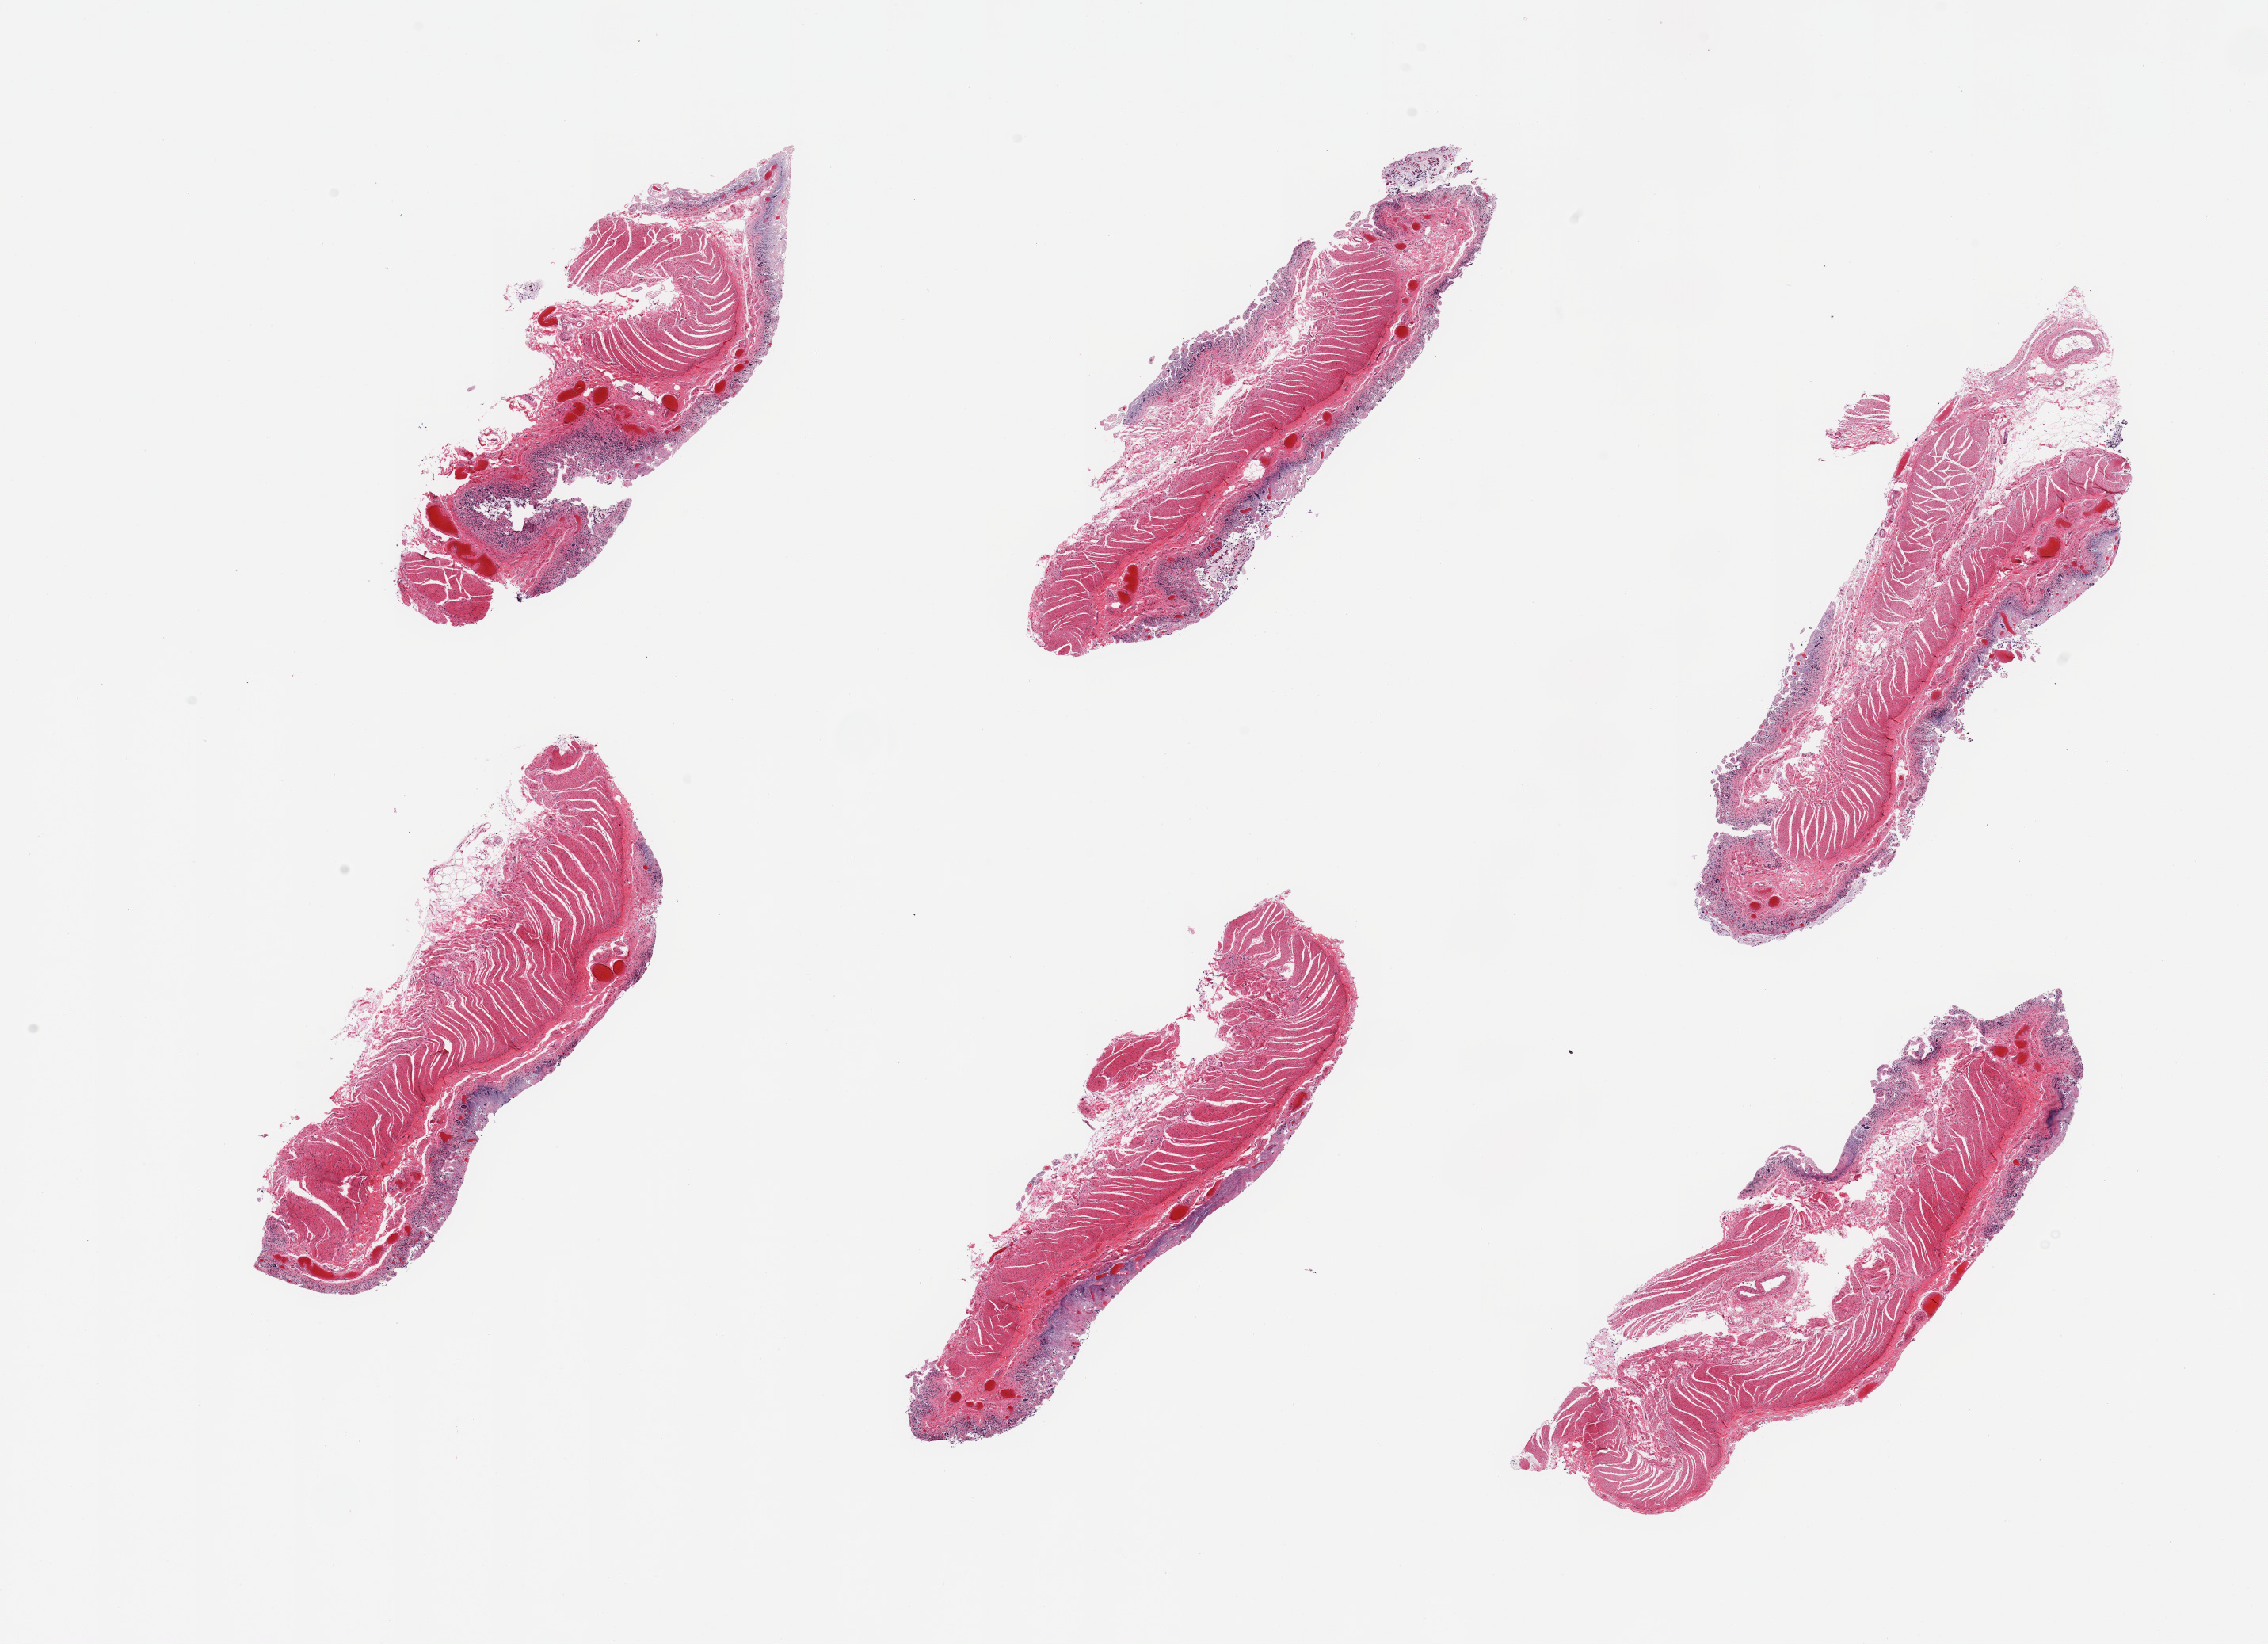
Haematoxylin and eosin whole-slide image, brightfield — low-resolution overview of the scanned area, about 22.6 x 16.4 mm. PAXgene-fixed paraffin-embedded (PFPE) section. Section of ileum (target tissue). Tissue donor sample.
Pathologist's review note for this sample: 6 pieces; mucosa autolyzed, minimal lymphoid tissue; muscularis propria present.